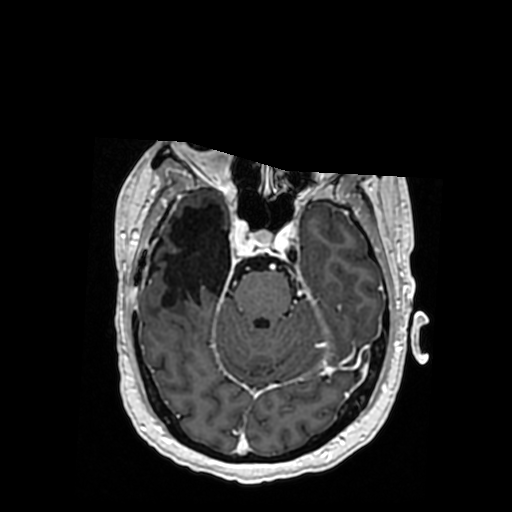
Brain MRI from a brain-tumour surgery series, one axial slice; position 234 of 364 along the scan axis; T1-weighted post-contrast; 0.5 mm slice thickness; 512 × 512 image matrix, field of view 260 × 260 mm. From the clinical record (not read from this slice): histopathology: Oligodendroglioma; WHO grade: 3; IDH mutation: yes; tumour location: Right Posterior Temporal Inferior Parietal.
Outlined on this slice (manually delineated by an expert):
- previous resection cavity: bounding box [x1, y1, x2, y2] px = [161, 205, 231, 307]